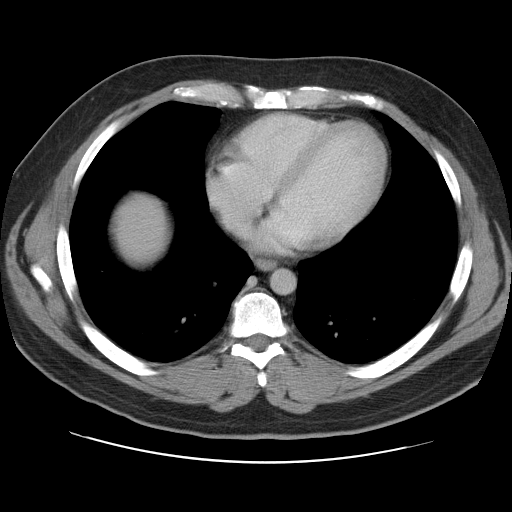
Contrast-enhanced abdominal CT, one axial slice. Intravenous contrast given. Soft-tissue window (W 400 / L 40 HU). 5 mm slice thickness. 512 × 512 image matrix, field of view 402 × 402 mm. Male patient, age 35 years. Case-level facts recorded for this patient, not image findings: diagnosis: colorectal cancer liver metastases, imaged before liver resection; multiple liver metastases: yes.
Outlined on this slice (outlined manually by an expert reader):
- liver: bounding box (x1, y1, x2, y2) in pixels: (114, 194, 166, 265)
- planned liver remnant (the part of the liver to remain after resection): (114, 194, 165, 265)